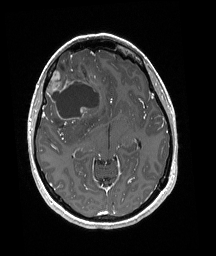
Brain MRI from a brain-tumour surgery series, one axial slice. Position 109 of 192 along the scan axis. T1-weighted post-contrast. 216 × 256 image matrix, field of view 211 × 250 mm. Case-level facts recorded for this patient, not image findings: histopathology: Oligodendroglioma; WHO grade: 3; IDH mutation: yes; tumour location: Right Frontal.
Outlined on this slice (manually delineated by an expert):
- tumour: bounding box [x1, y1, x2, y2] px = [46, 51, 99, 125]